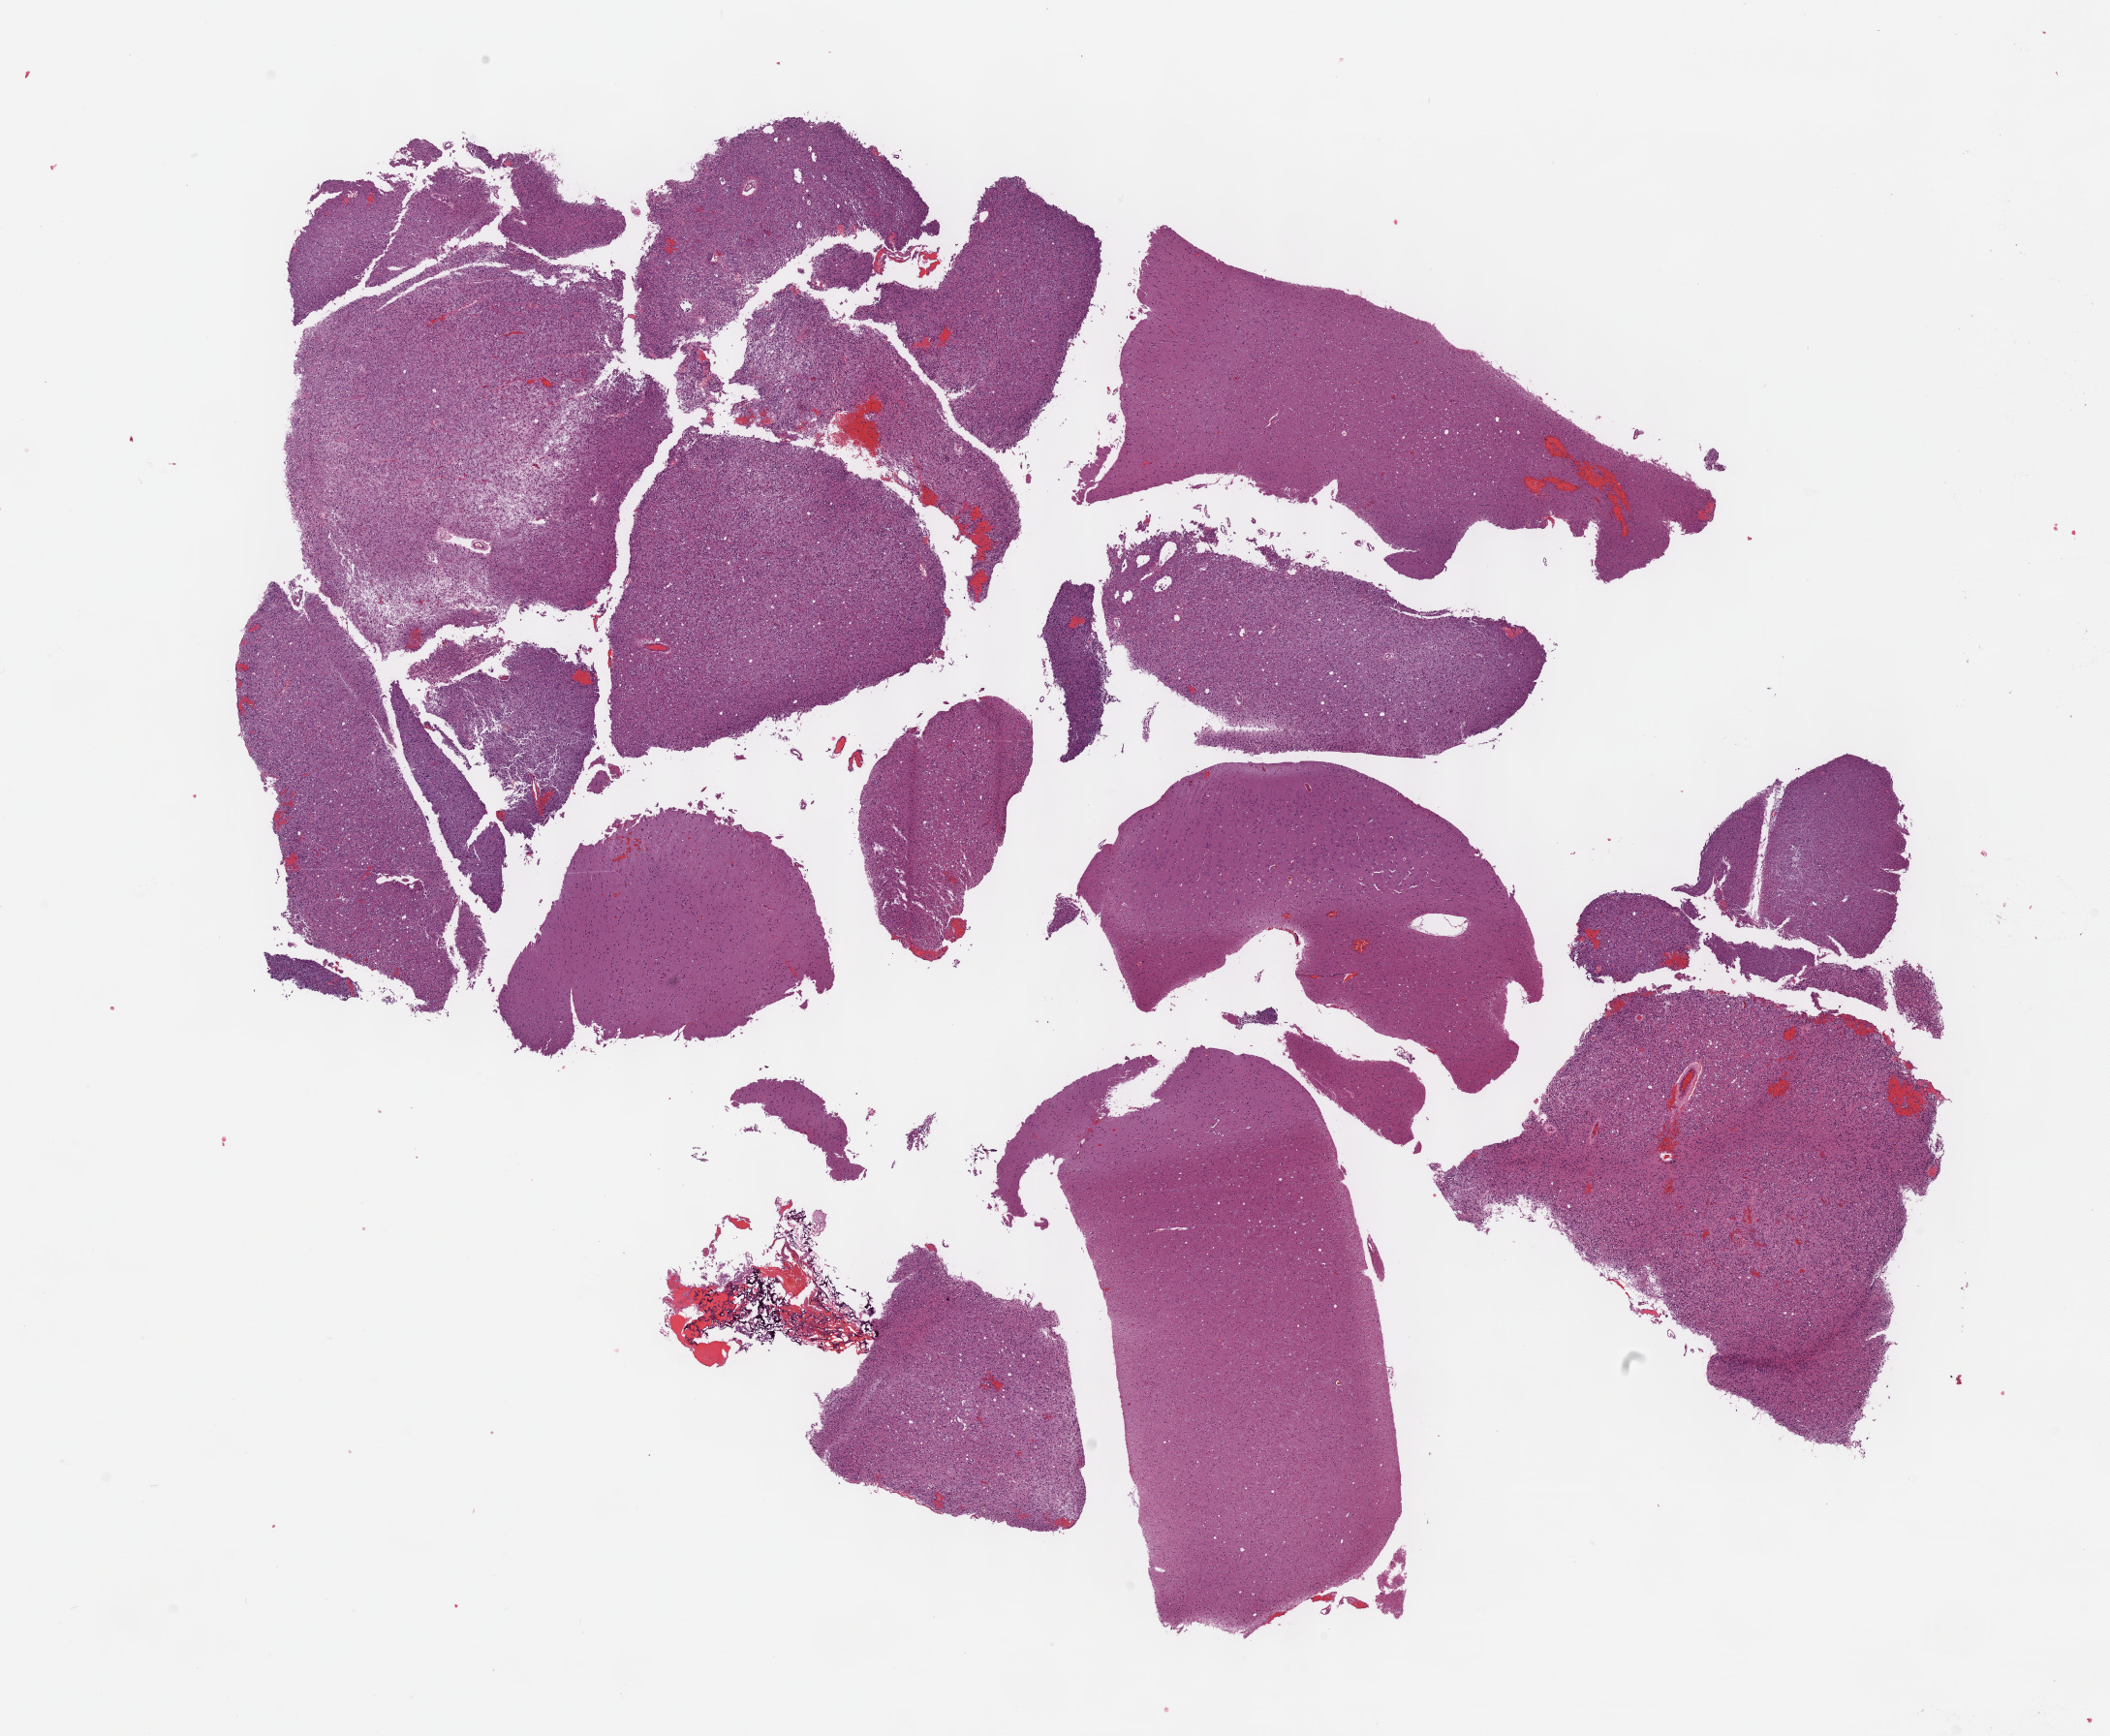
Hematoxylin and eosin (H&E) stained whole-slide image — low-resolution overview of the scanned area, about 17.6 x 14.5 mm; FFPE section; brain, primary tumour sample. Female, age 25 years at initial diagnosis. Histologic grade: G2 (moderately differentiated).
- diagnosis: Mixed glioma (cerebrum)